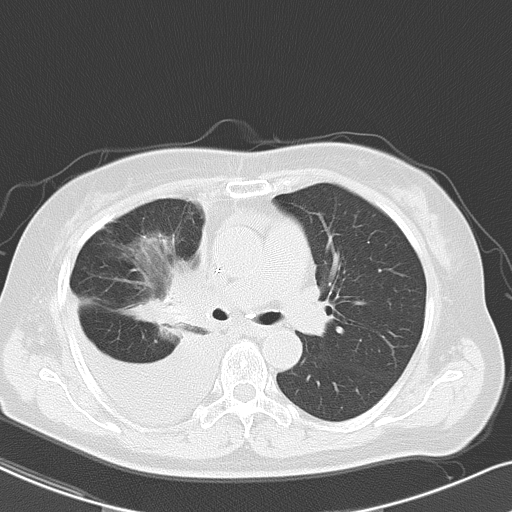
Chest CT, one axial slice. Slice 31 of 48 in the series (ordered by position). Reconstruction kernel B70f. 120 kVp. Lung window (W 1500 / L -600 HU). 5 mm slice thickness. 512 × 512 image matrix, field of view 328 × 328 mm. Patient: female, 69 years. From the clinical record (not read from this slice): clinical TNM (as recorded): T2a N0 M1c.
Annotated regions visible in this slice (bounding box drawn by a radiologist):
- lung tumour (recorded histology: adenocarcinoma): box from (x=149, y=224) to (x=222, y=334) px